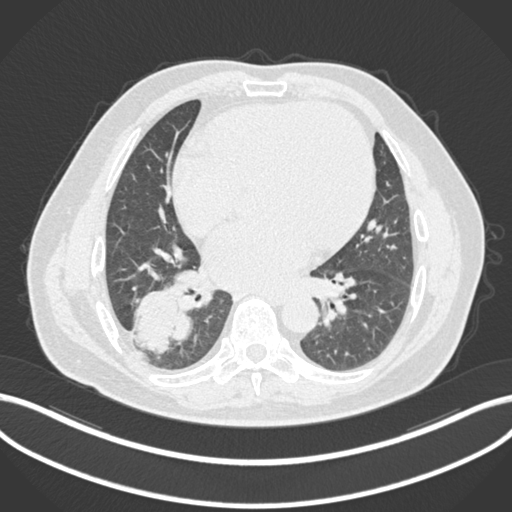
Chest CT, one axial slice. Slice 73 of 200 in the series (ordered by position). Reconstruction kernel B30f. 120 kVp. Lung window (W 1500 / L -600 HU). 1 mm slice thickness. 512 × 512 image matrix. Male patient, age 59 years.
Outlined on this slice (rectangle marked by the reading radiologist):
- lung tumour (recorded histology: adenocarcinoma): box from (x=131, y=288) to (x=195, y=356) px